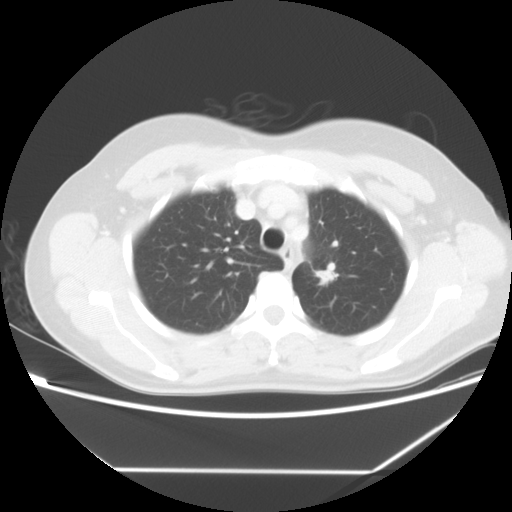
Chest CT, one axial slice. Slice 46 of 60 in the series (ordered by position). 140 kVp. Lung window (W 1500 / L -600 HU). 512 × 512 image matrix, field of view 367 × 367 mm. Patient: female, 43 years. From the clinical record (not read from this slice): clinical TNM (as recorded): T1c N0 M1b.
Structures marked on this image (bounding box drawn by a radiologist):
- lung tumour (recorded histology: adenocarcinoma): bounding box (x1, y1, x2, y2) in pixels: (314, 258, 337, 292)